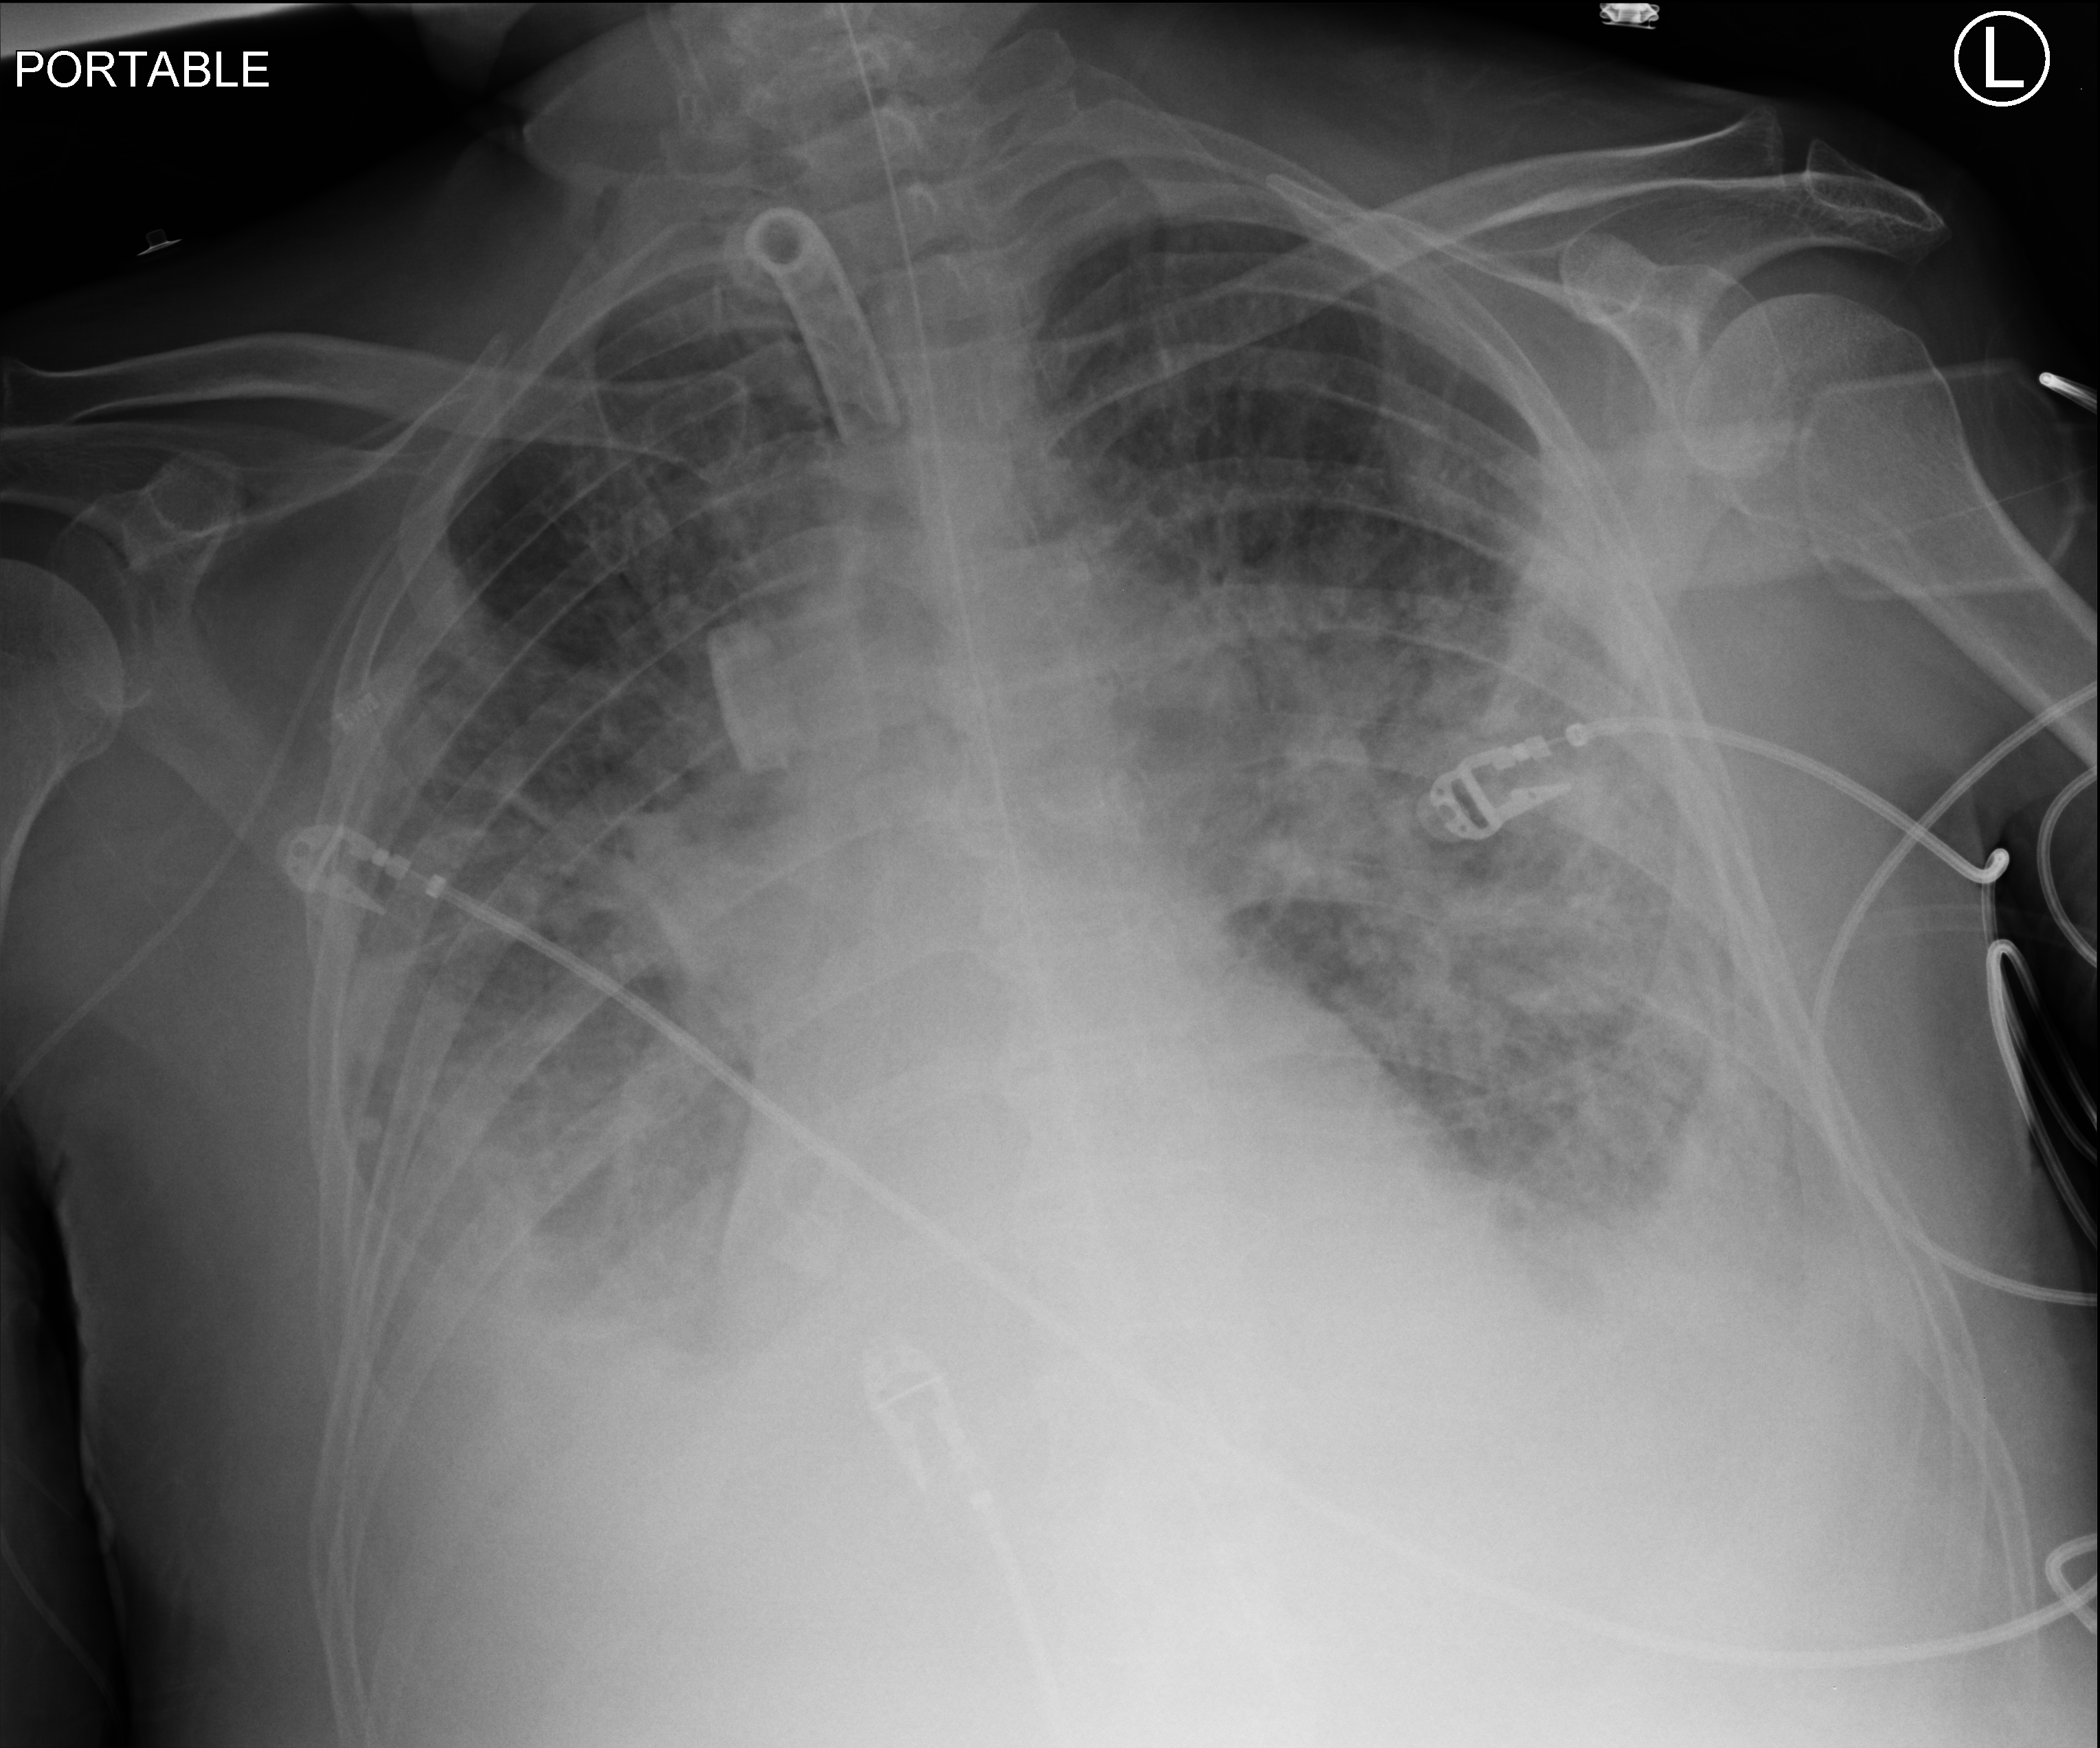
Bedside chest radiograph (computed radiography); anteroposterior (AP) projection. Patient hospitalised with COVID-19; male, aged 75–90 years.
Admission-level facts for this patient (not findings on this image; timing relative to this image not recorded):
- admitted to intensive care during this hospital stay: yes
- mechanically ventilated during this hospital stay: yes